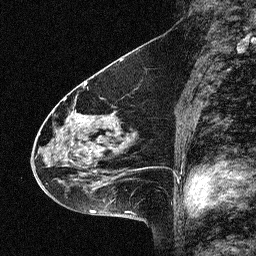
Breast MRI (dynamic contrast-enhanced), one sagittal slice. Position 30 of 64 along the scan axis. Dynamic contrast-enhanced study with each time point stored as its own series, time point 2 of 3 at this slice position (early post-contrast, ordered by acquisition time). 1.5 T. TE 4.5 ms, TR 11 ms. 256 × 256 image matrix, field of view 200 × 200 mm. Patient: female, 46 years. Case-level facts recorded for this patient, not image findings: setting: breast cancer imaged before/during neoadjuvant chemotherapy; receptor status: HER2-positive.
Outlined on this slice (semi-automatically segmented with operator editing):
- analysis volume of interest (the breast-tissue region the enhancement analysis was run in; not a lesion): box from (x=42, y=80) to (x=150, y=180) px
- tumour enhancement mask (voxels above the 90 % enhancement threshold inside the analysis volume of interest): (x=44, y=112)–(x=113, y=178)